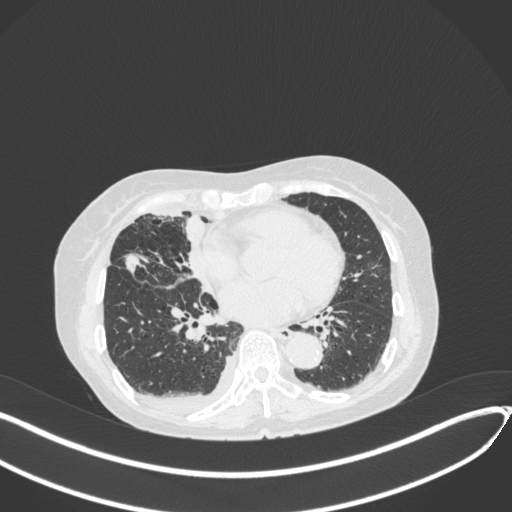
Chest CT, one axial slice. Position 165 of 418 along the scan axis. 120 kVp. Lung window (W 1500 / L -600 HU). 1 mm slice thickness. 512 × 512 image matrix, field of view 400 × 400 mm. Patient: female, 75 years. From the clinical record (not read from this slice): clinical TNM (as recorded): T2a N3 M0.
Annotated regions visible in this slice (rectangle marked by the reading radiologist):
- lung tumour (recorded histology: adenocarcinoma): bounding box <121,250,148,278> (left, top, right, bottom; pixels)